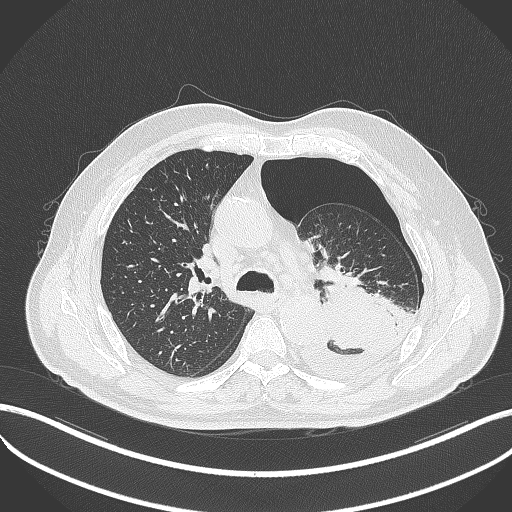
Chest CT, one axial slice; position 341 of 464 along the scan axis; 120 kVp; lung window (W 1500 / L -600 HU); 1 mm slice thickness; 512 × 512 image matrix, field of view 400 × 400 mm. Male patient, age 76 years. From the clinical record (not read from this slice): clinical TNM (as recorded): T3 N0 M1b.
Outlined on this slice (rectangle marked by the reading radiologist):
- lung tumour (recorded histology: adenocarcinoma): bounding box <322,269,401,352> (left, top, right, bottom; pixels)